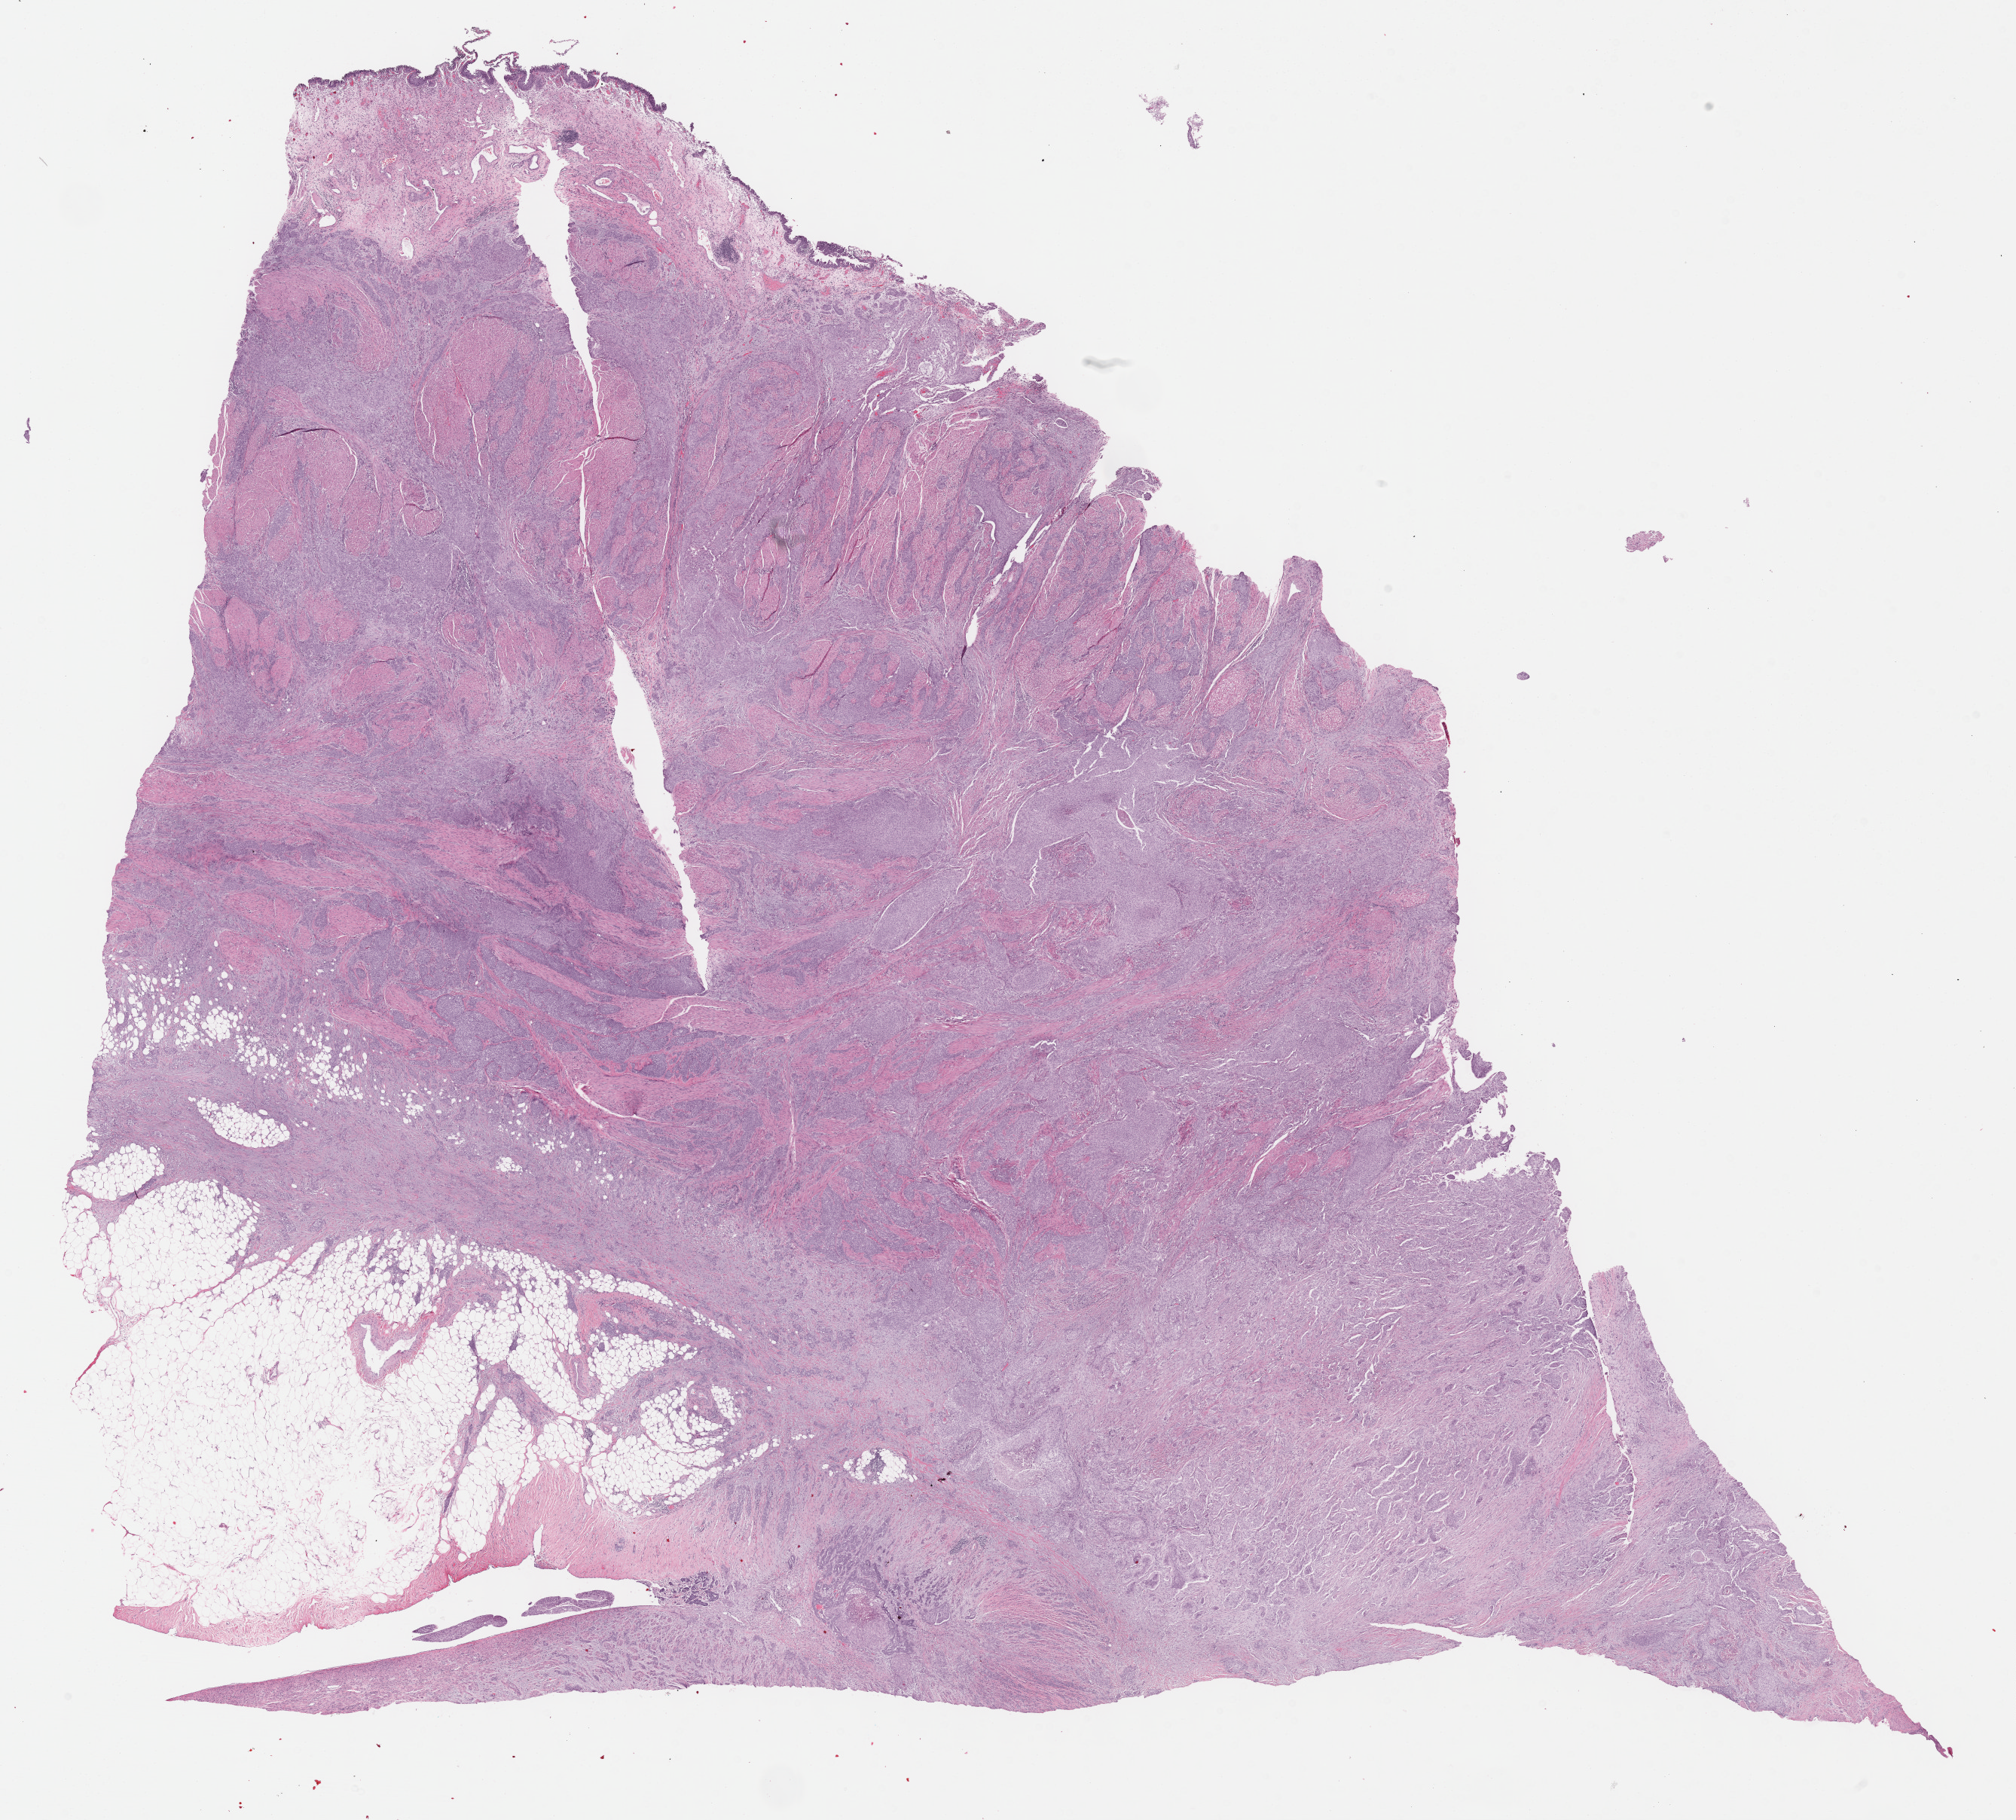
Digitized Hematoxylin and eosin (H&E) stained tissue section (whole slide), shown as a low-resolution overview of the whole scanned area (about 21.6 x 19.5 mm, acquisition: 40x scan). Formalin-fixed paraffin-embedded (FFPE) diagnostic section. Bladder, primary tumour sample. Female patient; age at initial diagnosis 74 years. Histologic grade: high grade.
- AJCC pathologic stage: IV (6th edition)
- pathologic diagnosis: Transitional cell carcinoma